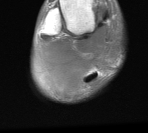
MRI of an extremity soft-tissue mass, one axial slice. Position 10 of 76 along the scan axis. MR volume resampled by the dataset authors to the PET/CT grid (not the native acquisition matrix). 3.27 mm slice thickness. 148 × 133 image matrix. Male patient. From the clinical record (not read from this slice): histological type: liposarcoma - round cell; grade: high; site of the primary tumour: right calf.
Annotated regions visible in this slice (expert contour drawn on MRI and transferred to this co-registered scan by the dataset authors):
- gross tumour volume (mass): bounding box (x1, y1, x2, y2) in pixels: (33, 25, 119, 97)